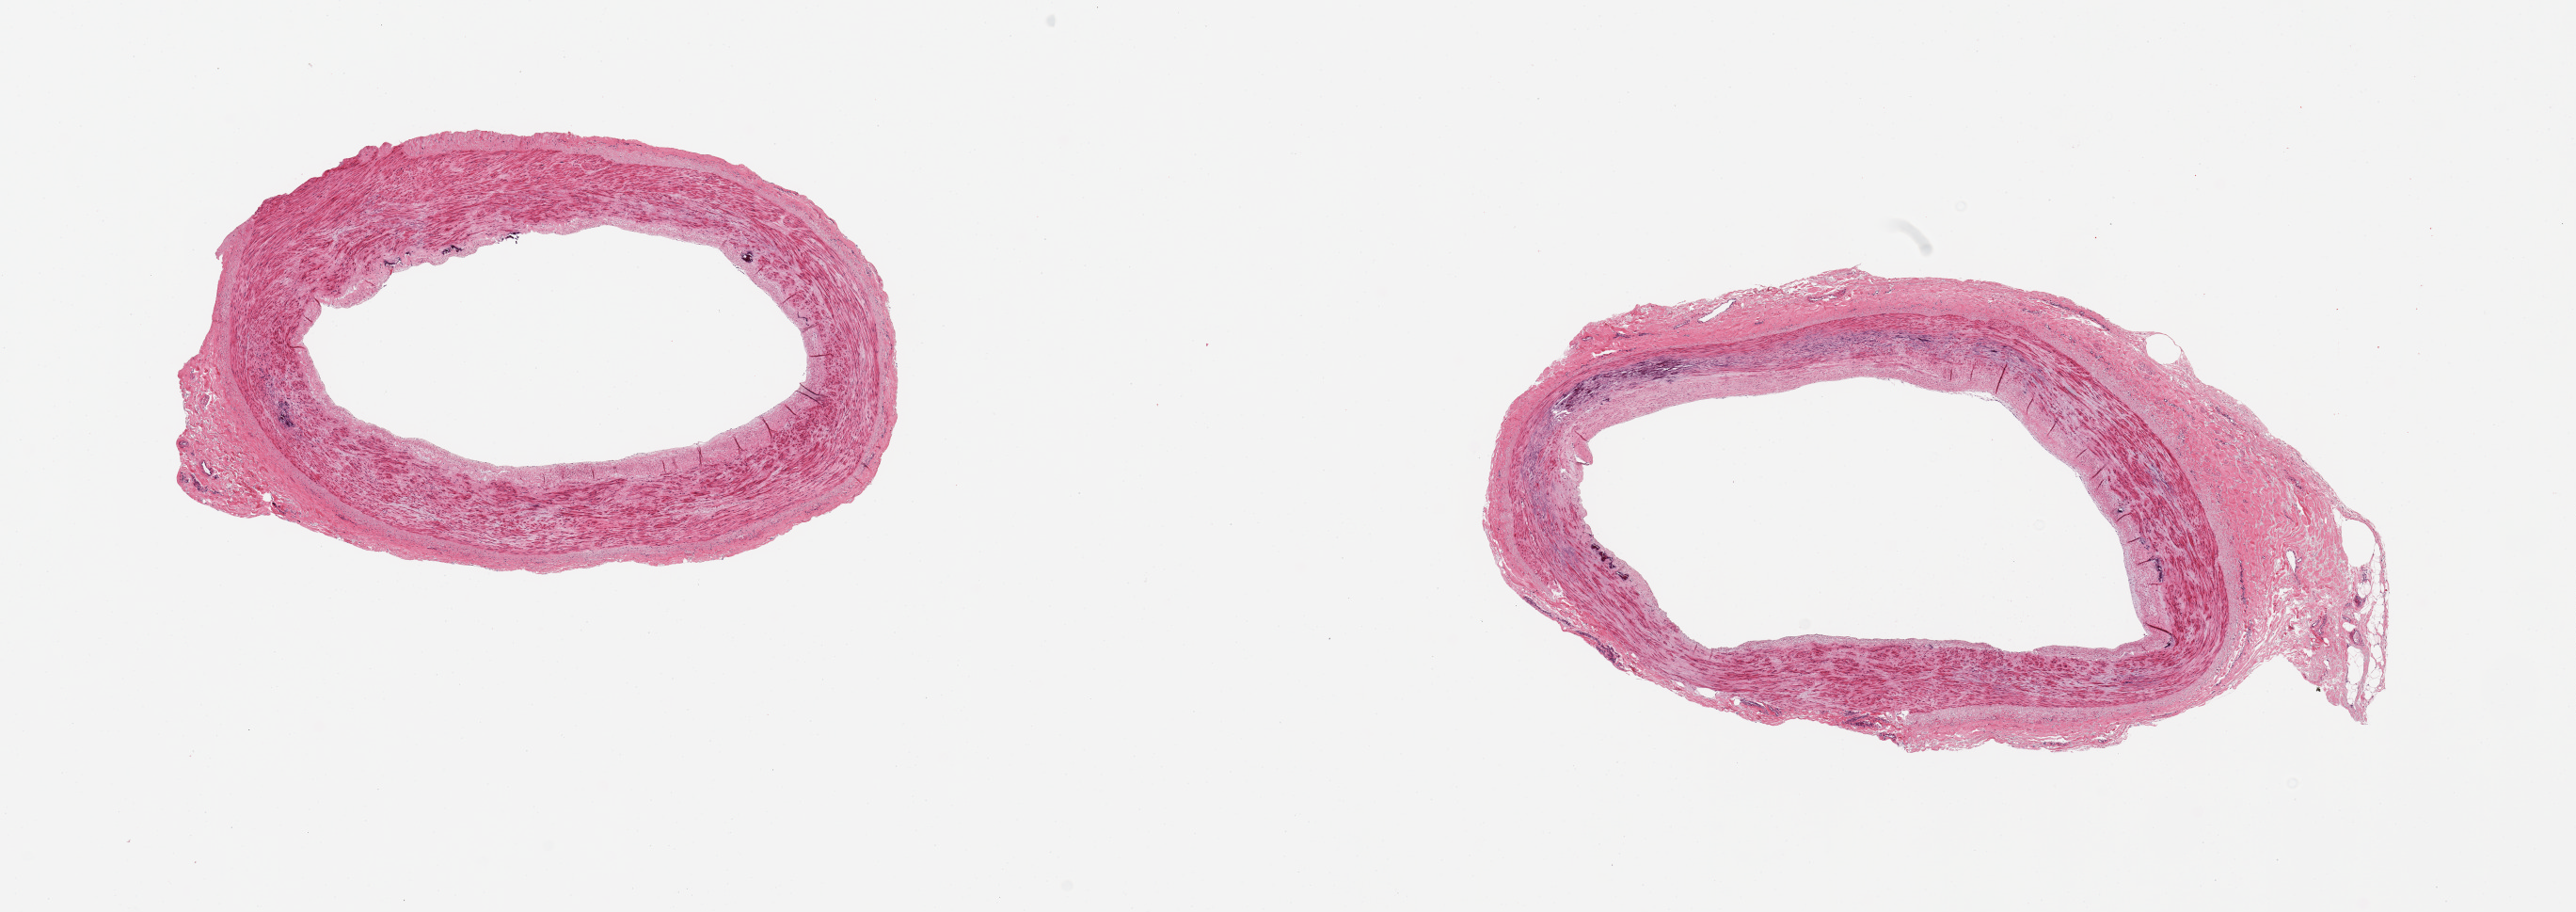
Whole-slide image, haematoxylin and eosin stain — low-resolution overview of the scanned area, about 21.7 x 7.7 mm (from a 20x scan). Donor sex: female.
Specimen: PAXgene-fixed paraffin-embedded (PFPE) section; target tissue: tibial artery; tissue donor sample.